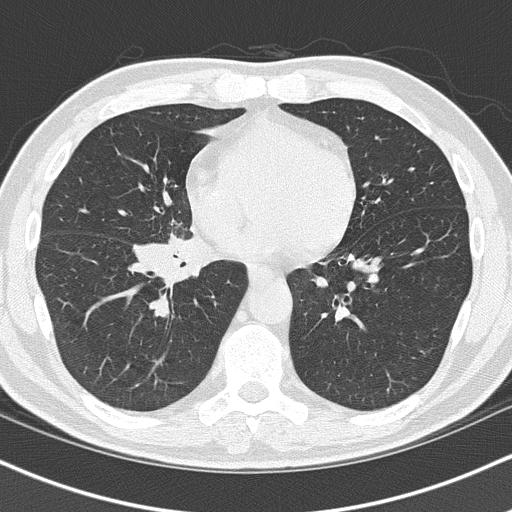
Low-dose screening chest CT, axial slice, baseline screening round, lung window (W 1500 / L -600 HU), 2 mm slice thickness, lung (sharp) reconstruction kernel (B50f), 120 kVp, 512 × 512 image matrix. Male, age 55 years at enrolment. Current smoker at enrolment.
Lesion marked by an expert reader, bounding box (x1, y1, x2, y2) in pixels: (132, 226, 240, 307). Screening reader's record for this exam (one nodule recorded; not confirmed to be the boxed lesion): non-calcified nodule or mass ≥4 mm, right lower lobe, 6 × 5 mm, spiculated (stellate) margins, soft tissue attenuation. Participant outcome: lung cancer diagnosed 21 days after this screen — carcinoma, NOS, right hilum, stage IB (AJCC 6th edition), 67 mm at pathology.